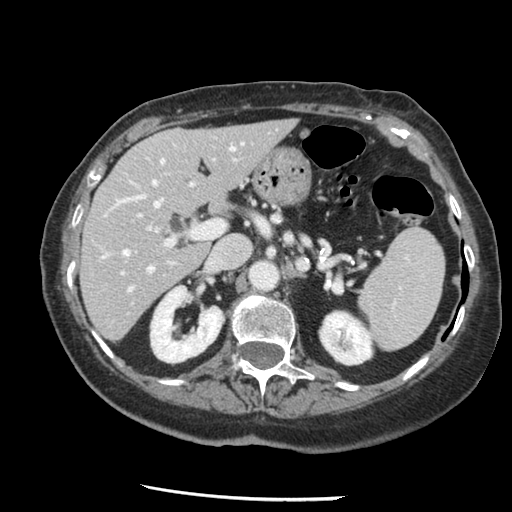
Contrast-enhanced abdominal CT, one axial slice. Position 80 of 148 along the scan axis. Intravenous contrast given. Soft-tissue window (W 400 / L 40 HU). 2.5 mm slice thickness. 512 × 512 image matrix, field of view 330 × 330 mm. Female patient, age 85 years. From the clinical record (not read from this slice): diagnosis: colorectal cancer liver metastases, imaged before liver resection; multiple liver metastases: no; largest metastasis: 0.9 cm; disease in both lobes: no.
Outlined on this slice (outlined manually by an expert reader):
- hepatic veins: bounding box [x1, y1, x2, y2] px = [103, 143, 177, 291]
- liver: [81, 120, 295, 340]
- planned liver remnant (the part of the liver to remain after resection): [81, 120, 295, 340]
- portal vein (with intrahepatic branches): [138, 146, 230, 247]